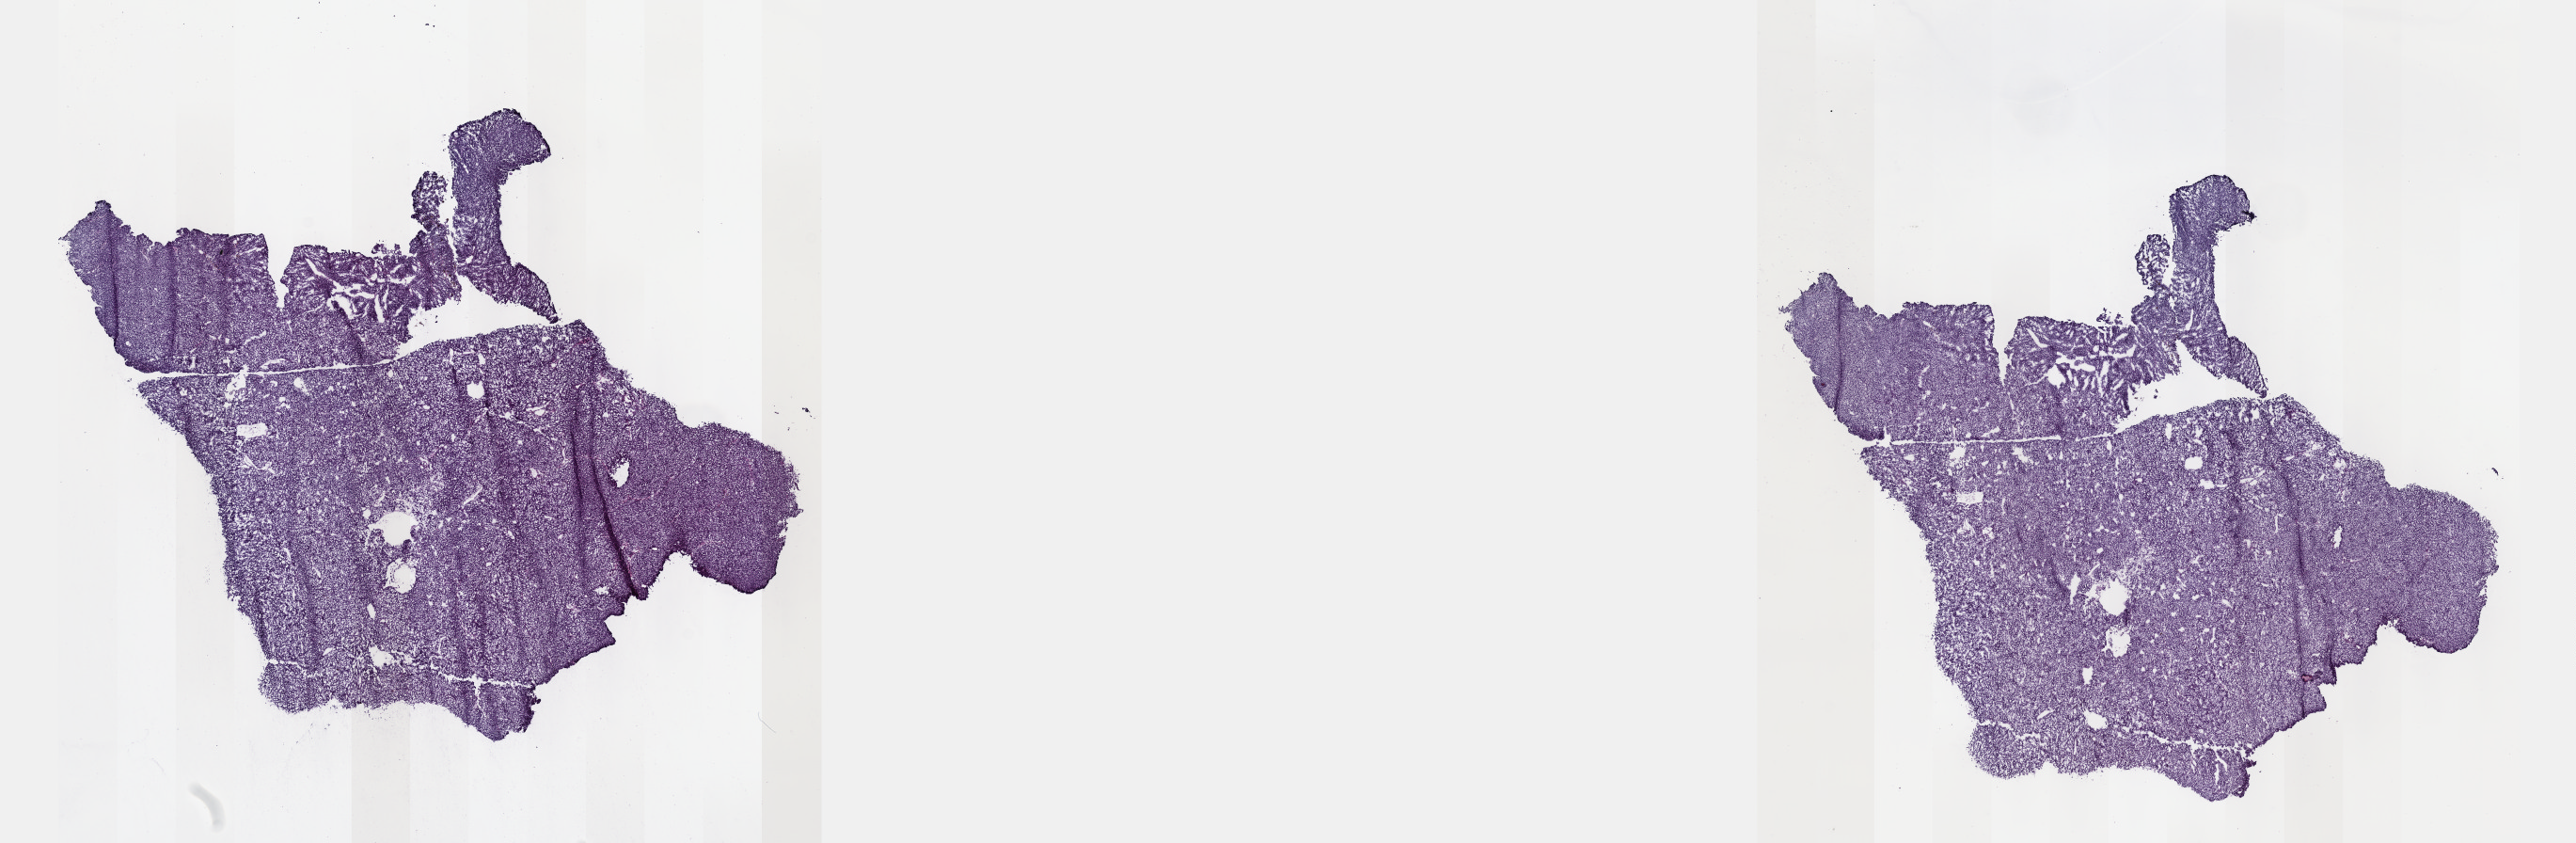
H&E-stained whole-slide image, low-resolution overview of the scanned area, about 22.1 x 7.2 mm (slide scanned at 40x), frozen section from the top of the tissue portion, sample: primary tumour, uvea. Female, age 54 years at initial diagnosis.
Histologic diagnosis: Mixed epithelioid and spindle cell melanoma.